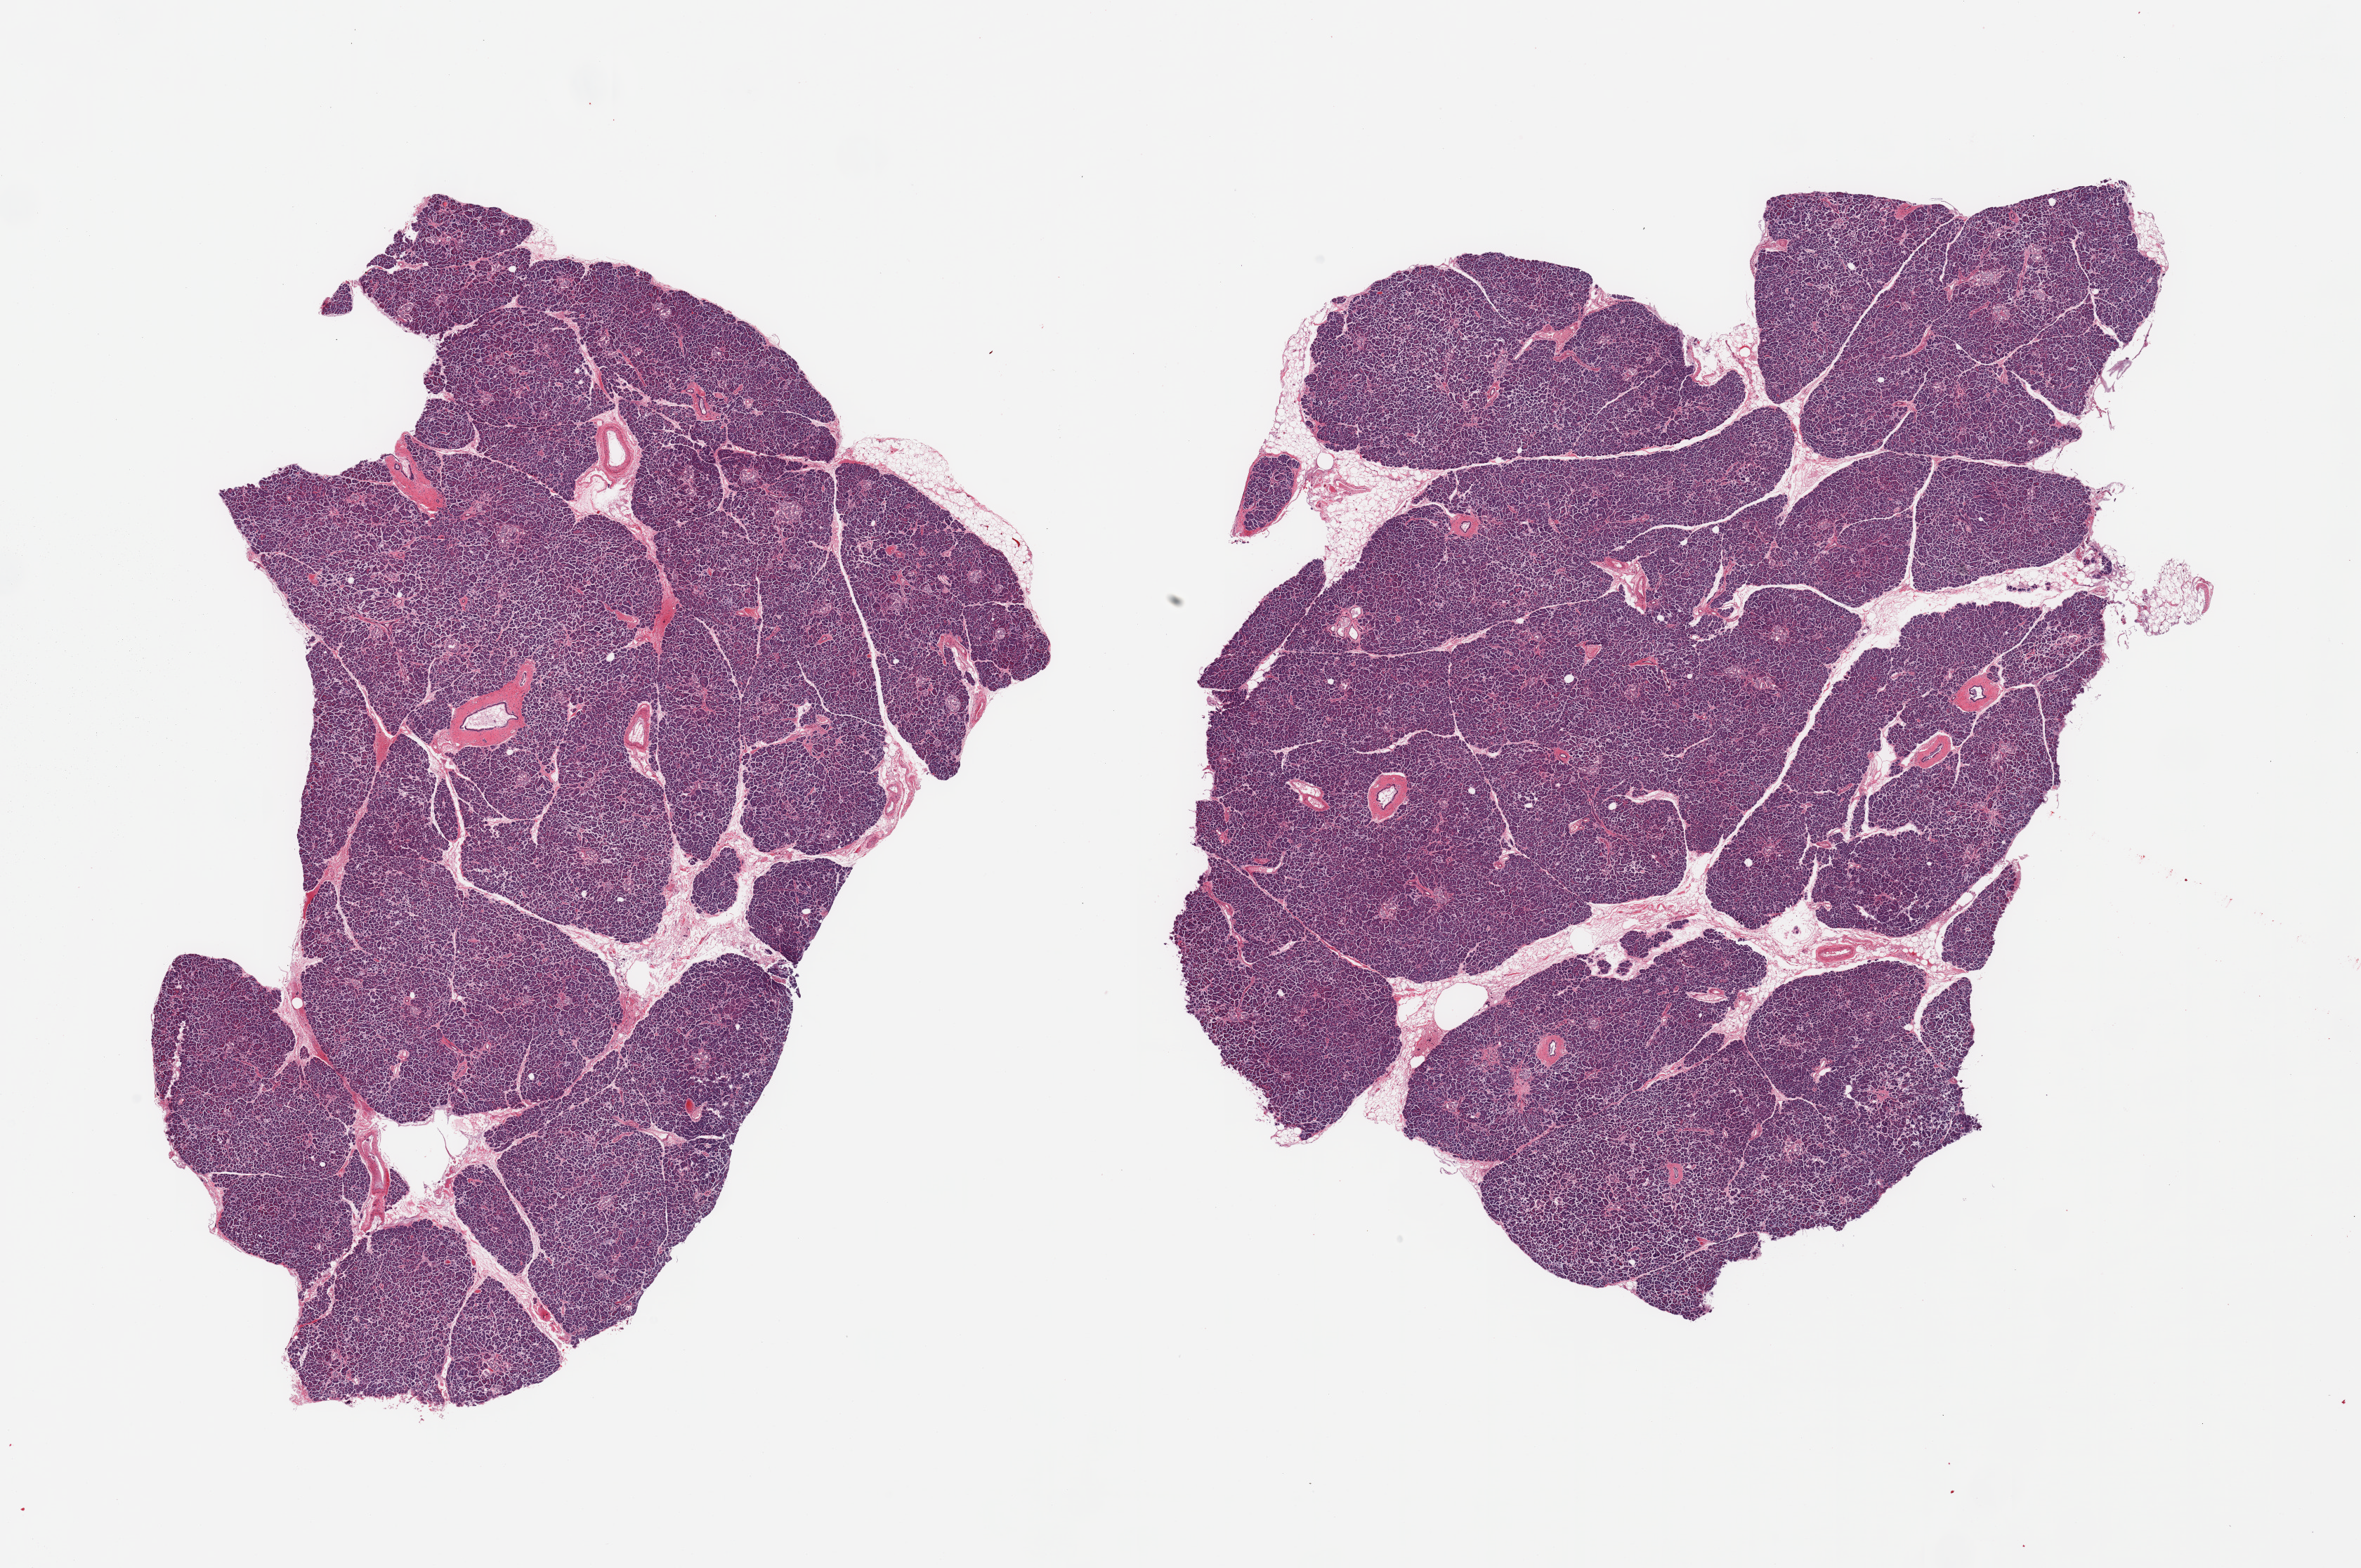
Digitized H&E-stained section, shown as a low-resolution overview of the whole scanned area (about 26.6 x 17.7 mm). PAXgene-fixed, paraffin-embedded tissue. Section of pancreas (target tissue). Tissue donor sample.
Reviewer comment on this tissue sample: 2 pieces; up to ~15% internal fat with conspicuous islets.